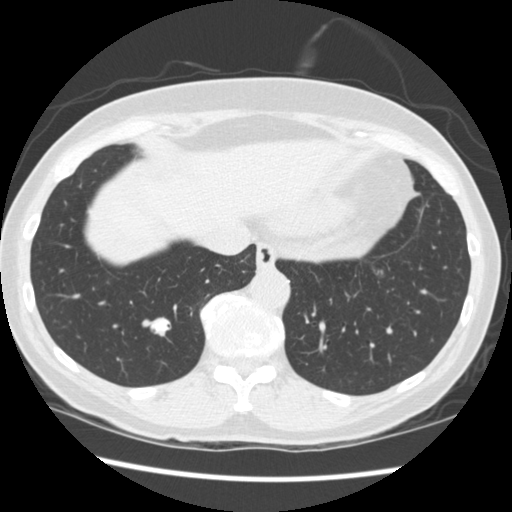
Low-dose screening chest CT, one axial slice; position 67 of 262 along the scan axis; 120 kVp; lung window (W 1500 / L -600 HU); 512 × 512 image matrix, field of view 340 × 340 mm.
Outlined on this slice (manually delineated by an expert):
- lesion 1 (tumor, lower lobe of right lung): bounding box (x1, y1, x2, y2) in pixels: (151, 318, 170, 336)